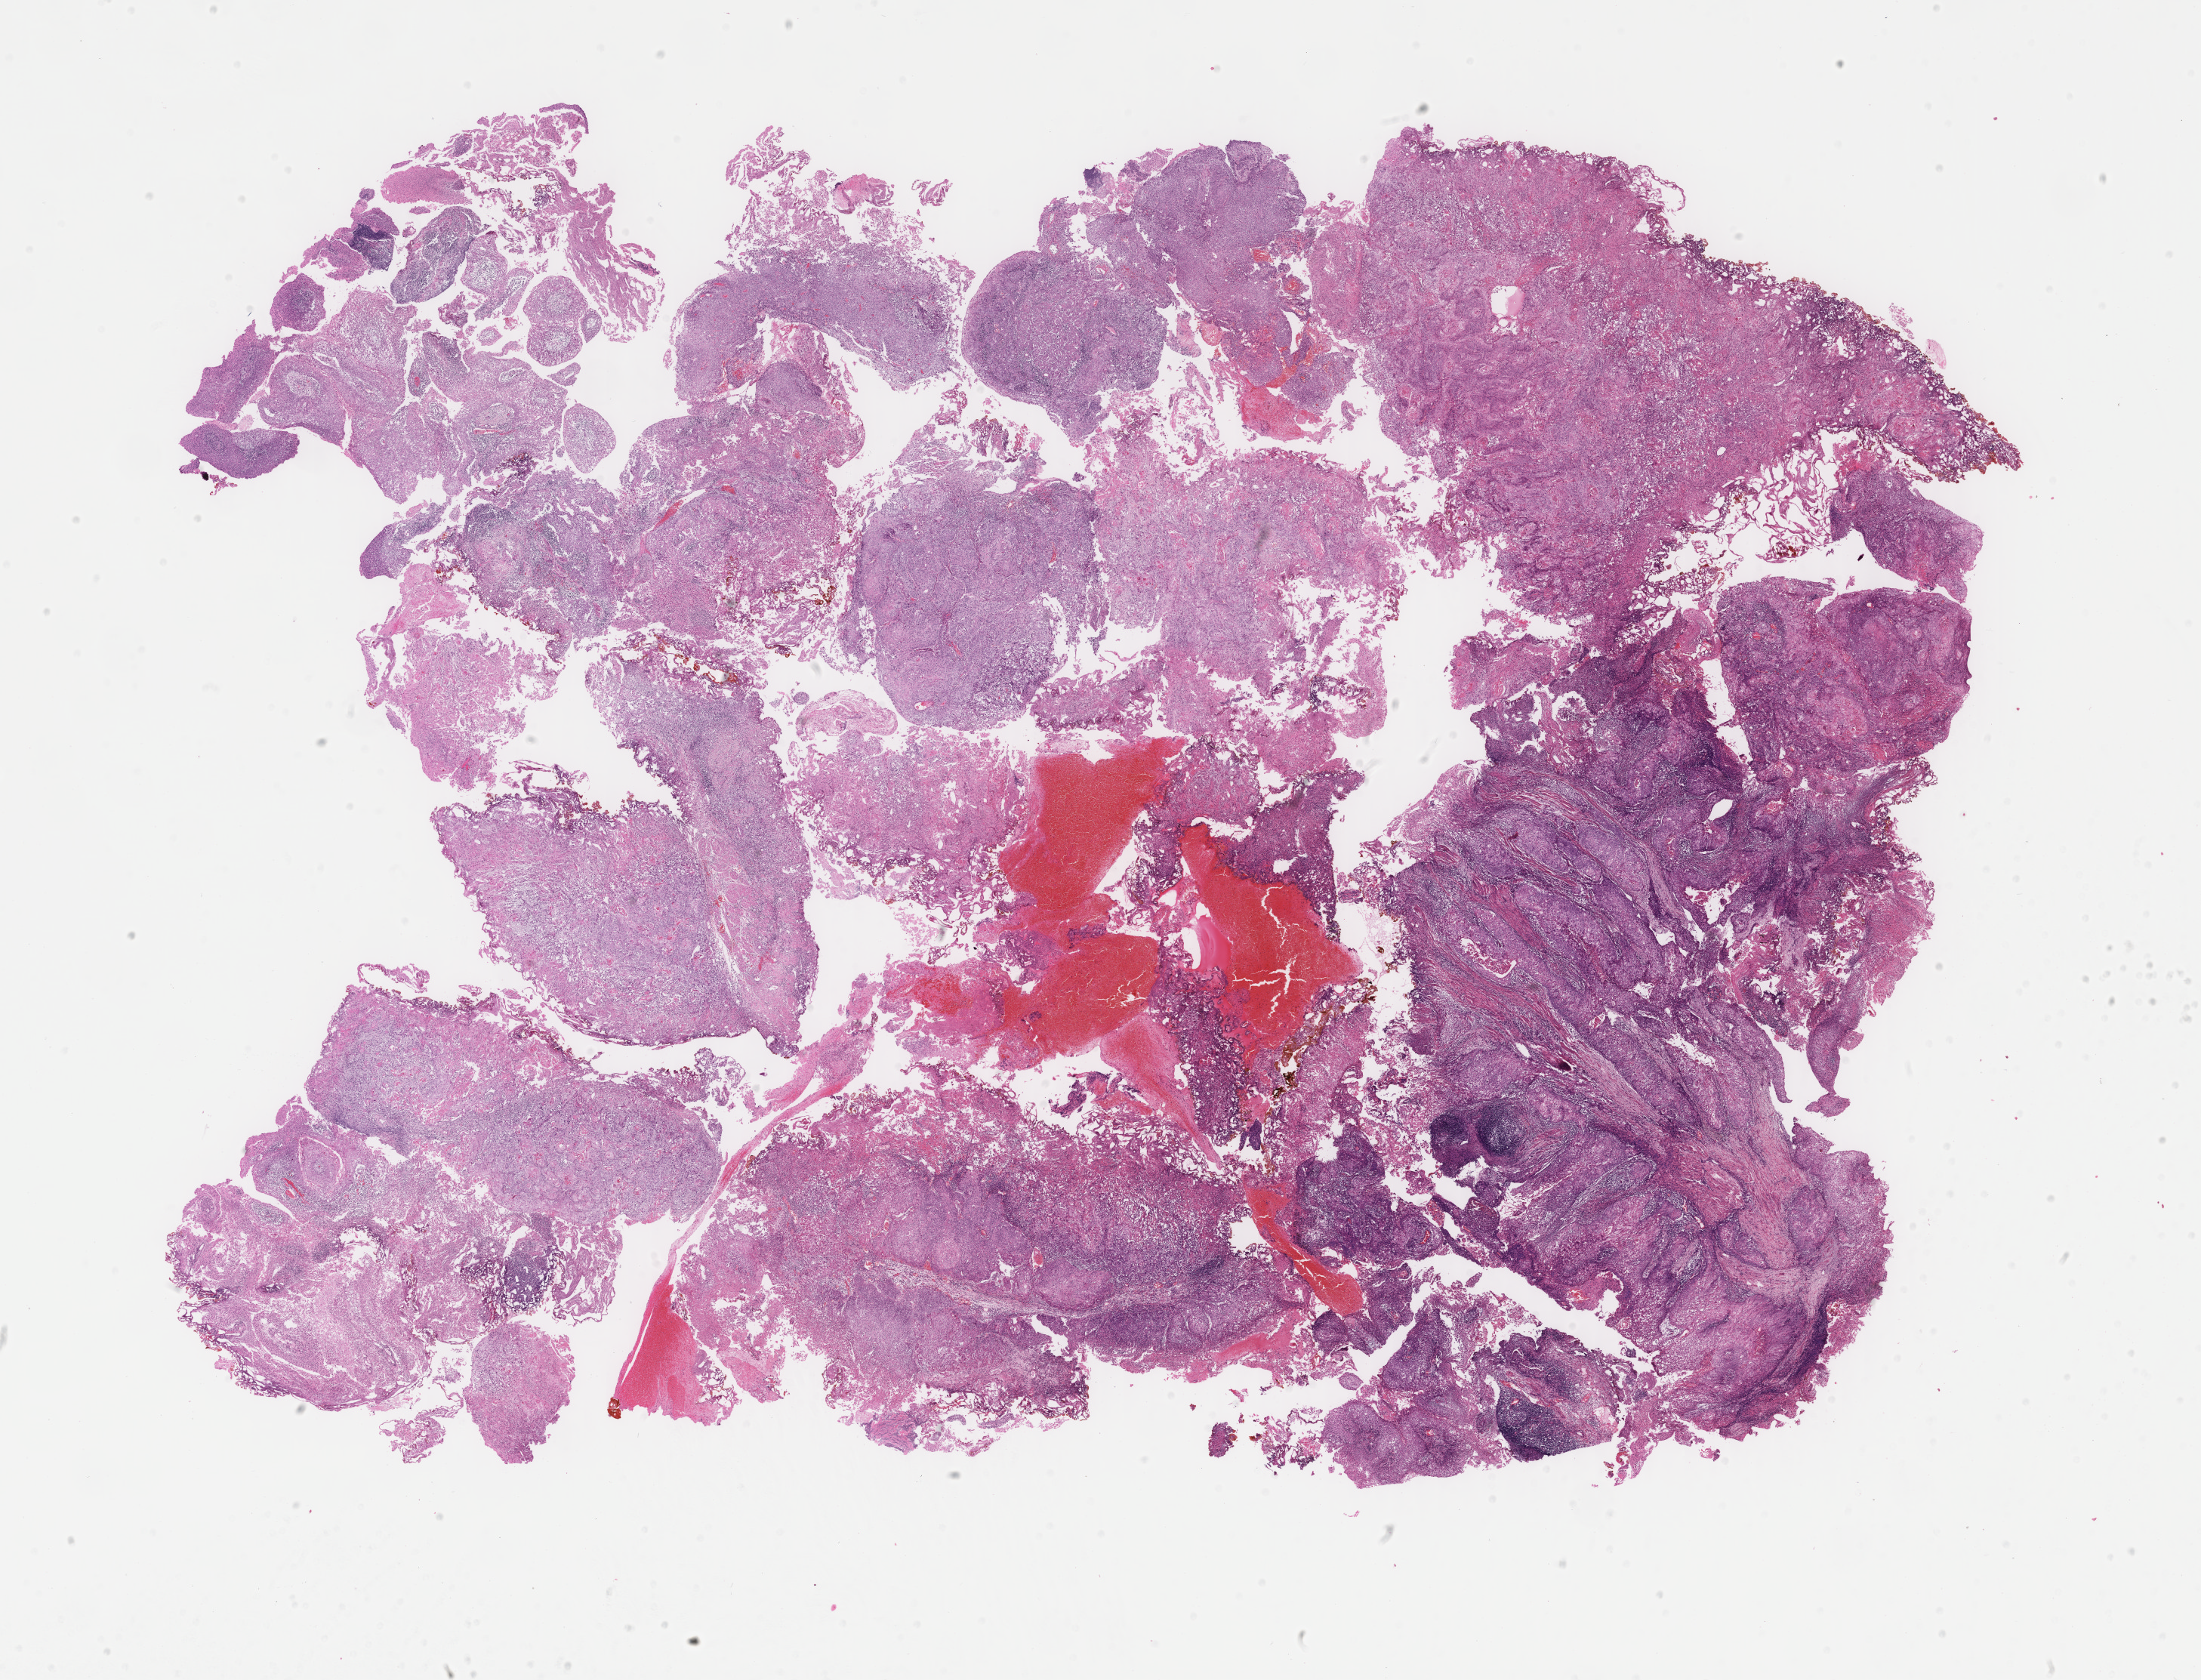
Digitized H&E tissue section (whole slide) — a low-resolution overview of the entire scanned area, about 23.1 x 17.7 mm (acquisition: 40x scan); formalin-fixed paraffin-embedded (FFPE) diagnostic section; sample: primary tumour, bladder. Patient: female, age at initial diagnosis 56 years. Histologic grade: high grade.
Diagnosis: Transitional cell carcinoma. AJCC pathologic stage: II.